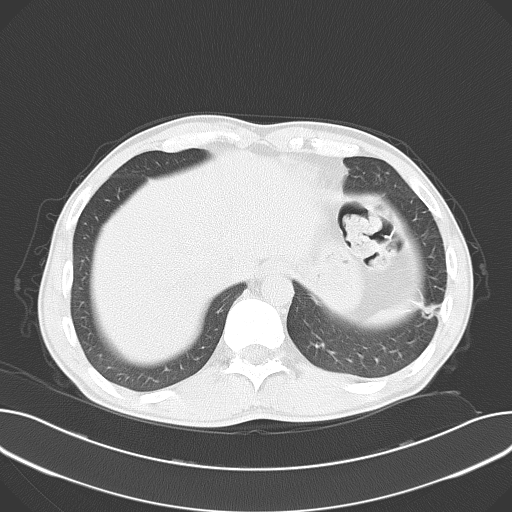
Chest CT, one axial slice; position 14 of 62 along the scan axis; 120 kVp; lung window (W 1500 / L -600 HU); 5 mm slice thickness; 512 × 512 image matrix. Male patient, age 44 years. Case-level facts recorded for this patient, not image findings: clinical TNM (as recorded): T1c N0 M1b.
Structures marked on this image (bounding box drawn by a radiologist):
- lung tumour (recorded histology: adenocarcinoma): box from (x=419, y=301) to (x=447, y=323) px